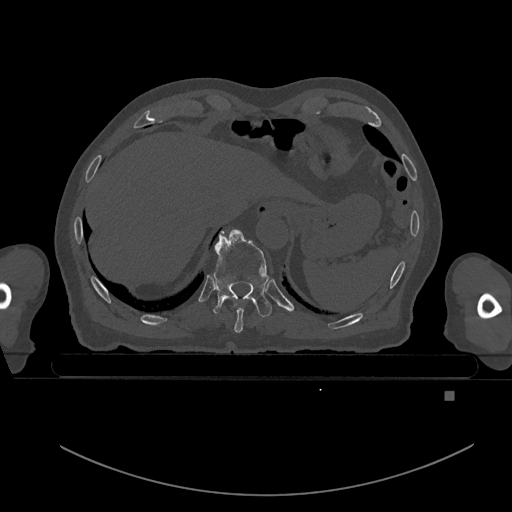
CT including the spine, one axial slice. Slice 107 of 969 in the series (ordered by position). Bone window (W 1800 / L 400 HU). 0.5 mm slice thickness. 512 × 512 image matrix. Patient: male, 82 years. Case-level facts recorded for this patient, not image findings: primary cancer: prostate.
Structures marked on this image (semi-automatic segmentation, software-assisted and operator-edited):
- T10 vertebra: bounding box <213,229,272,317> (left, top, right, bottom; pixels)
- T9 vertebra: <234,302,245,333>